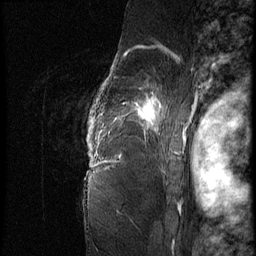
Breast MRI (dynamic contrast-enhanced), one sagittal slice. Slice 56 of 62 in the series (ordered by position). 3 images stored at this slice position (order not interpretable as contrast timing). 1.5 T. TE 4.2 ms, TR 9 ms. 2.5 mm slice thickness. 256 × 256 image matrix. Patient: female, 56 years. Case-level facts recorded for this patient, not image findings: setting: breast cancer imaged before/during neoadjuvant chemotherapy; receptor status: HER2-positive.
Structures marked on this image (semi-automatically segmented with operator editing):
- analysis volume of interest (the breast-tissue region the enhancement analysis was run in; not a lesion): box from (x=84, y=75) to (x=181, y=153) px
- tumour enhancement mask (voxels above the 140 % enhancement threshold inside the analysis volume of interest): (x=89, y=76)–(x=161, y=149)